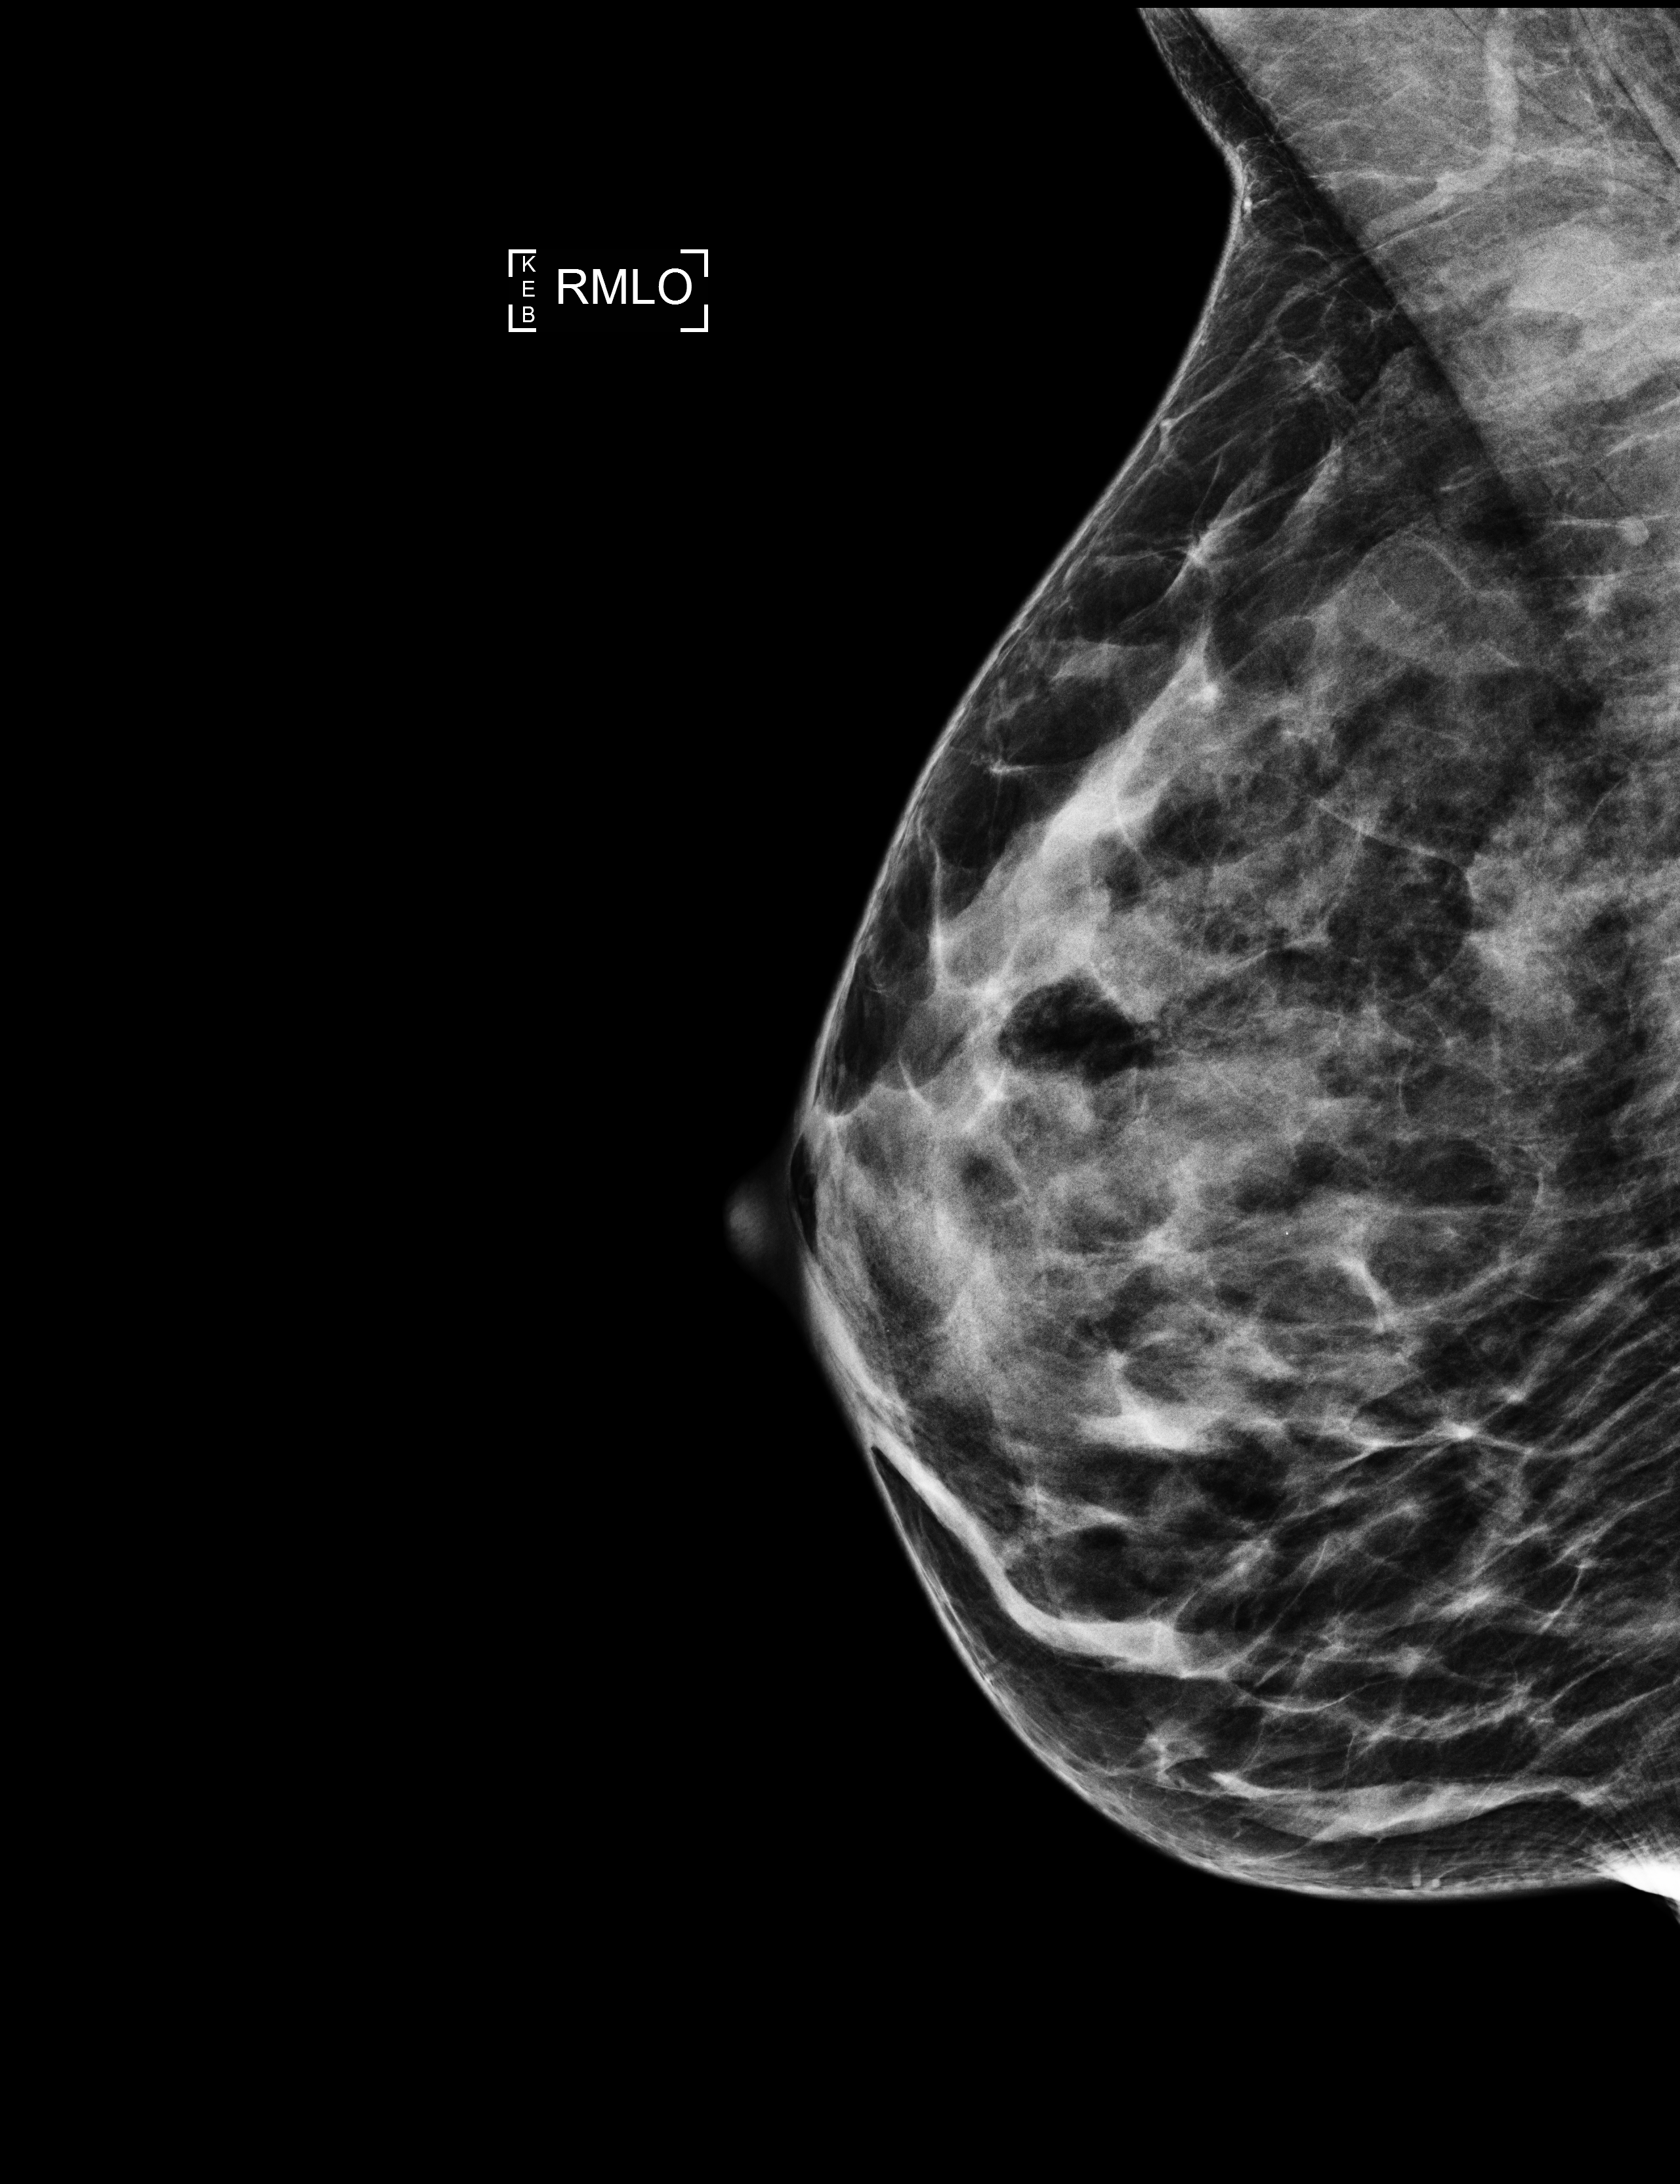
Diagnostic work-up study. Female patient, age 56 years.
Image type: full-field digital mammogram. Breast: right. Projection: MLO view.